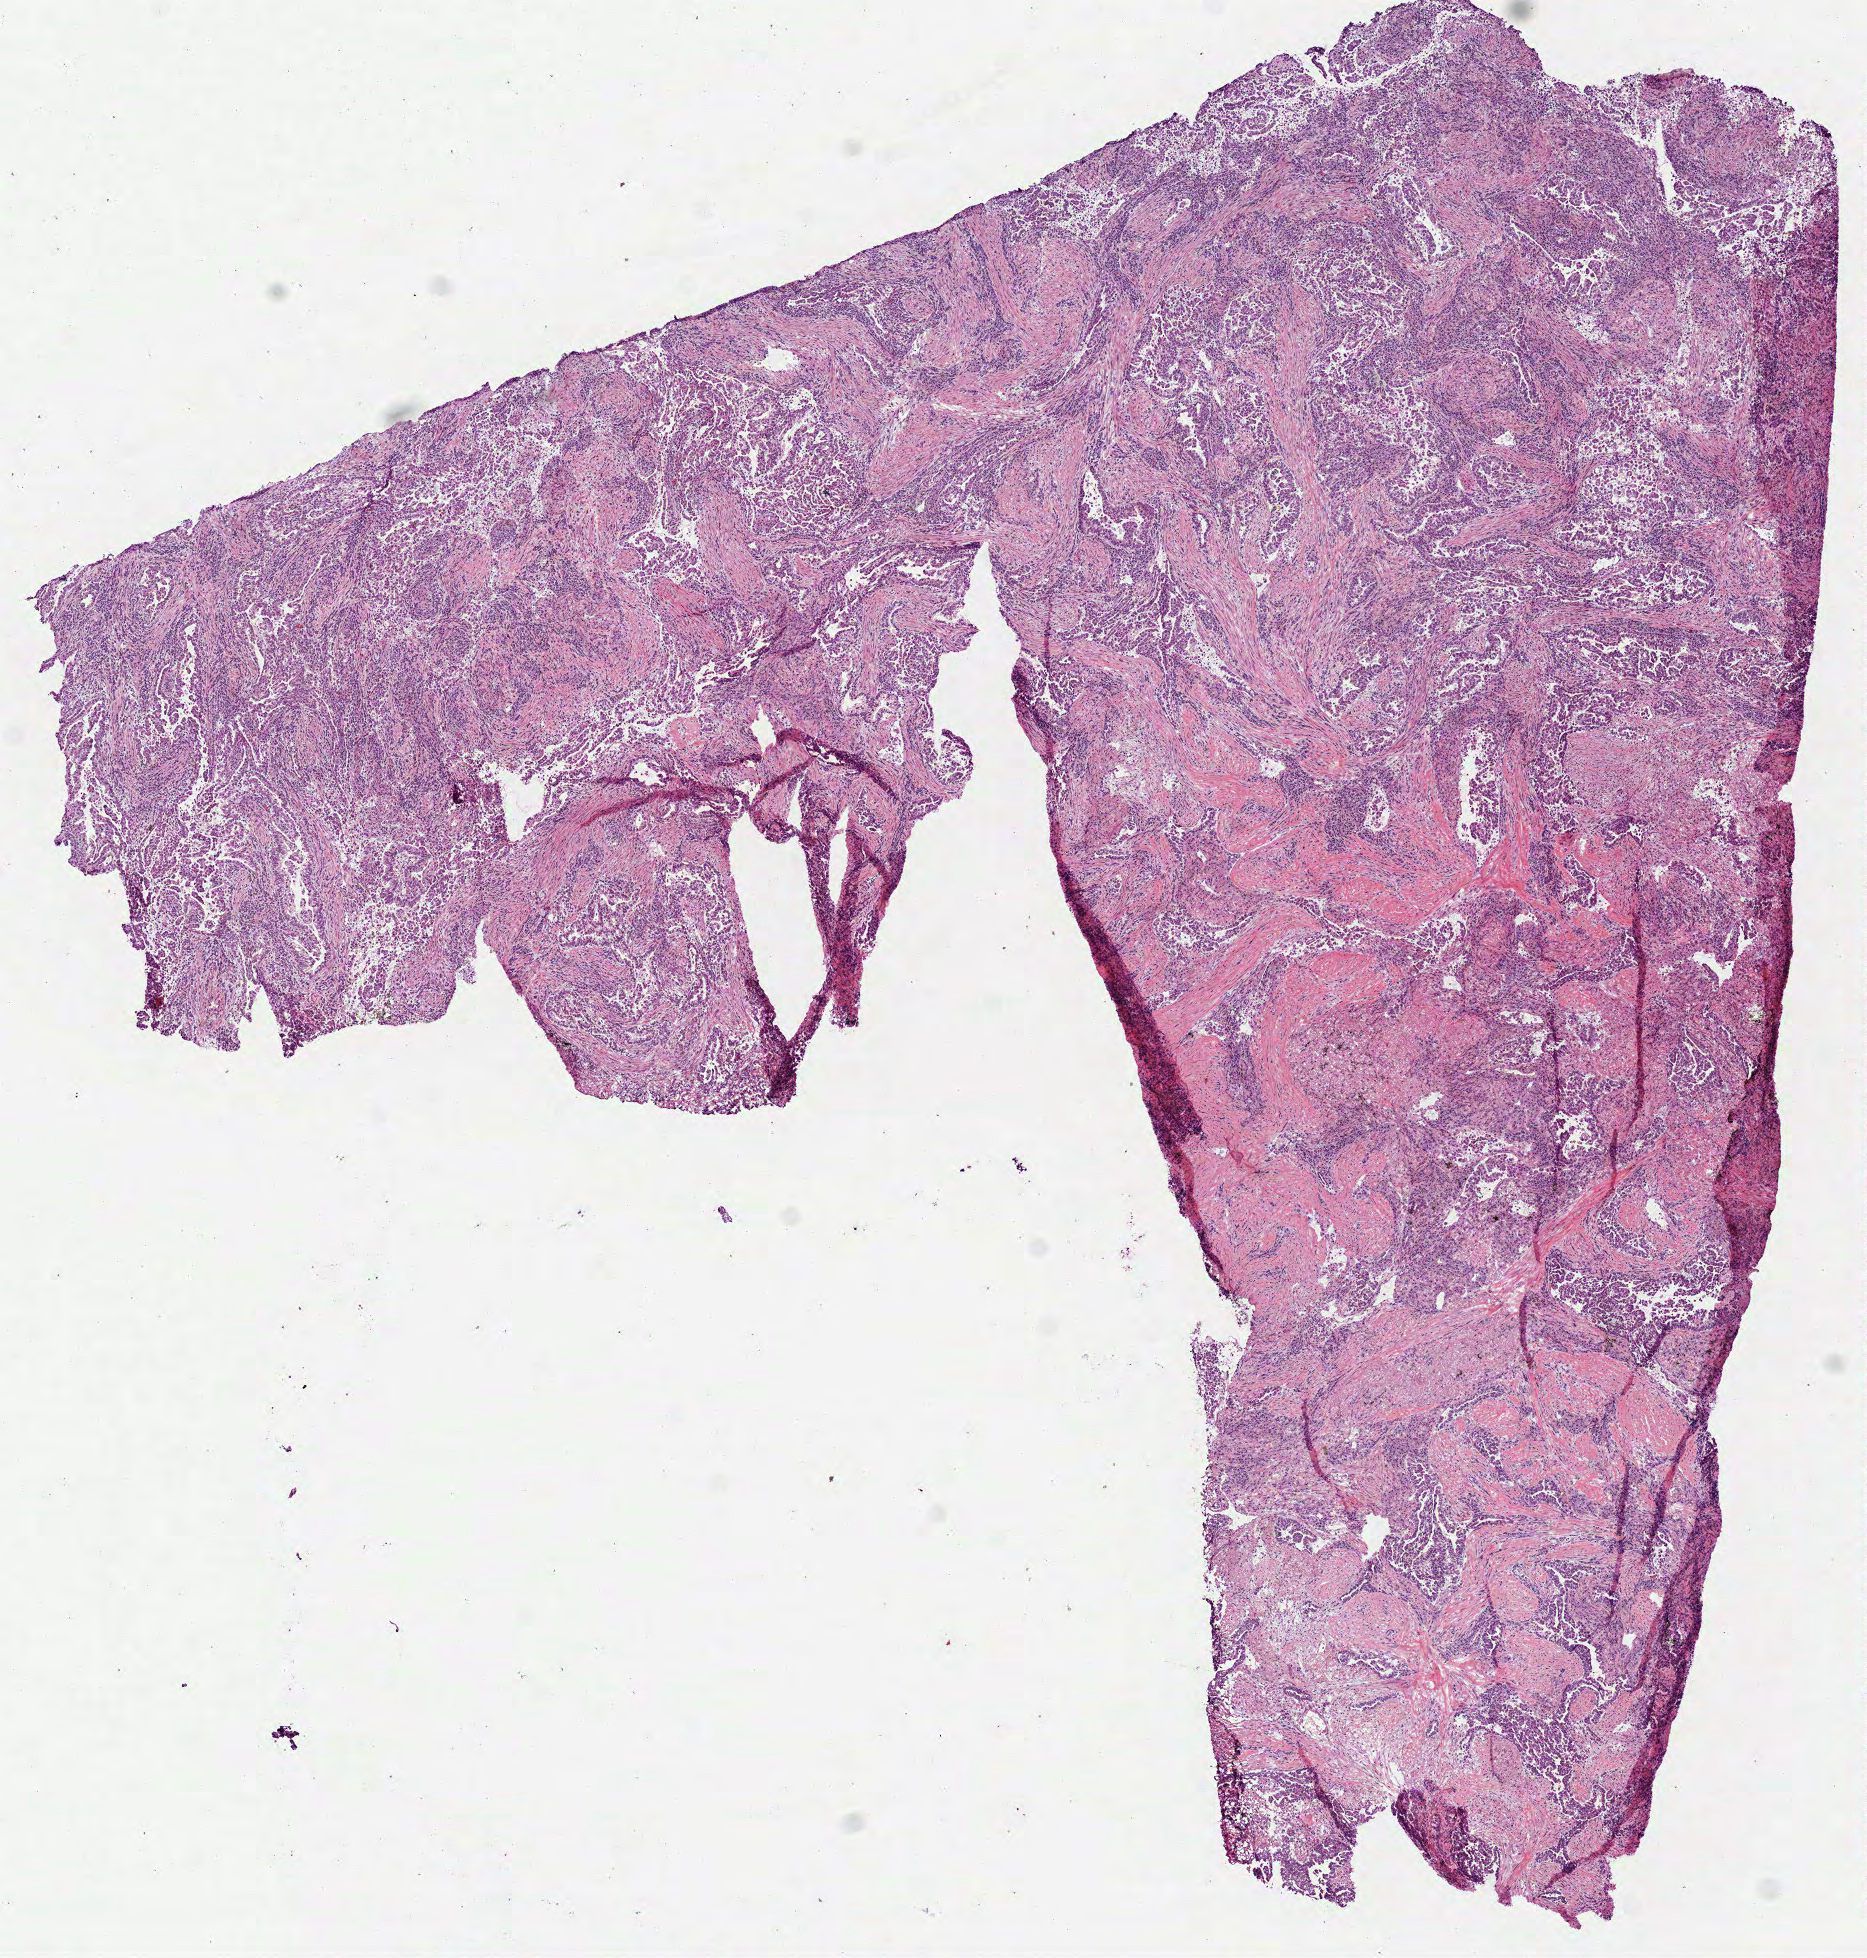
Whole-slide histology image, H&E — low-resolution overview of the scanned area, about 7.5 x 7.9 mm (acquisition: 40x scan). Frozen section. Sample: primary tumour, lung. Patient: male, age at initial diagnosis 63 years. Pathologist review of this section (percent, as recorded): tumour cells 70%, tumour nuclei 80%, normal cells 0%, stromal cells 30%, necrosis 0%.
Laterality: right. Pathologic diagnosis: Adenocarcinoma, NOS. AJCC pathologic stage: IB.